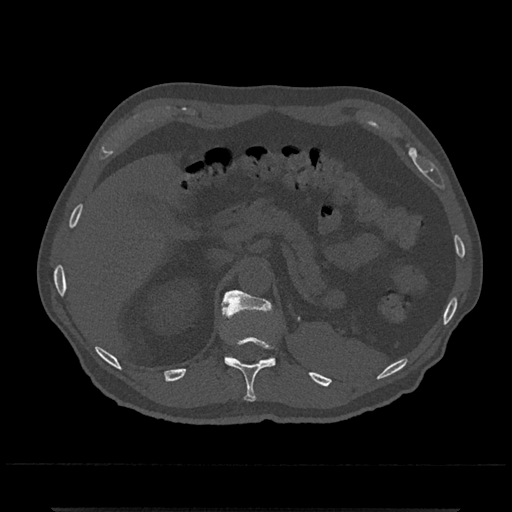
CT including the spine, one axial slice; position 470 of 797 along the scan axis; reconstruction kernel Br40s/3; bone window (W 1800 / L 400 HU); 0.5 mm slice thickness; 512 × 512 image matrix, field of view 393 × 393 mm. Male patient, age 67 years. From the clinical record (not read from this slice): primary cancer: prostate.
Structures marked on this image (semi-automatically segmented with operator editing):
- T11 vertebra: bounding box <222,303,276,402> (left, top, right, bottom; pixels)
- T12 vertebra: <221,290,274,360>